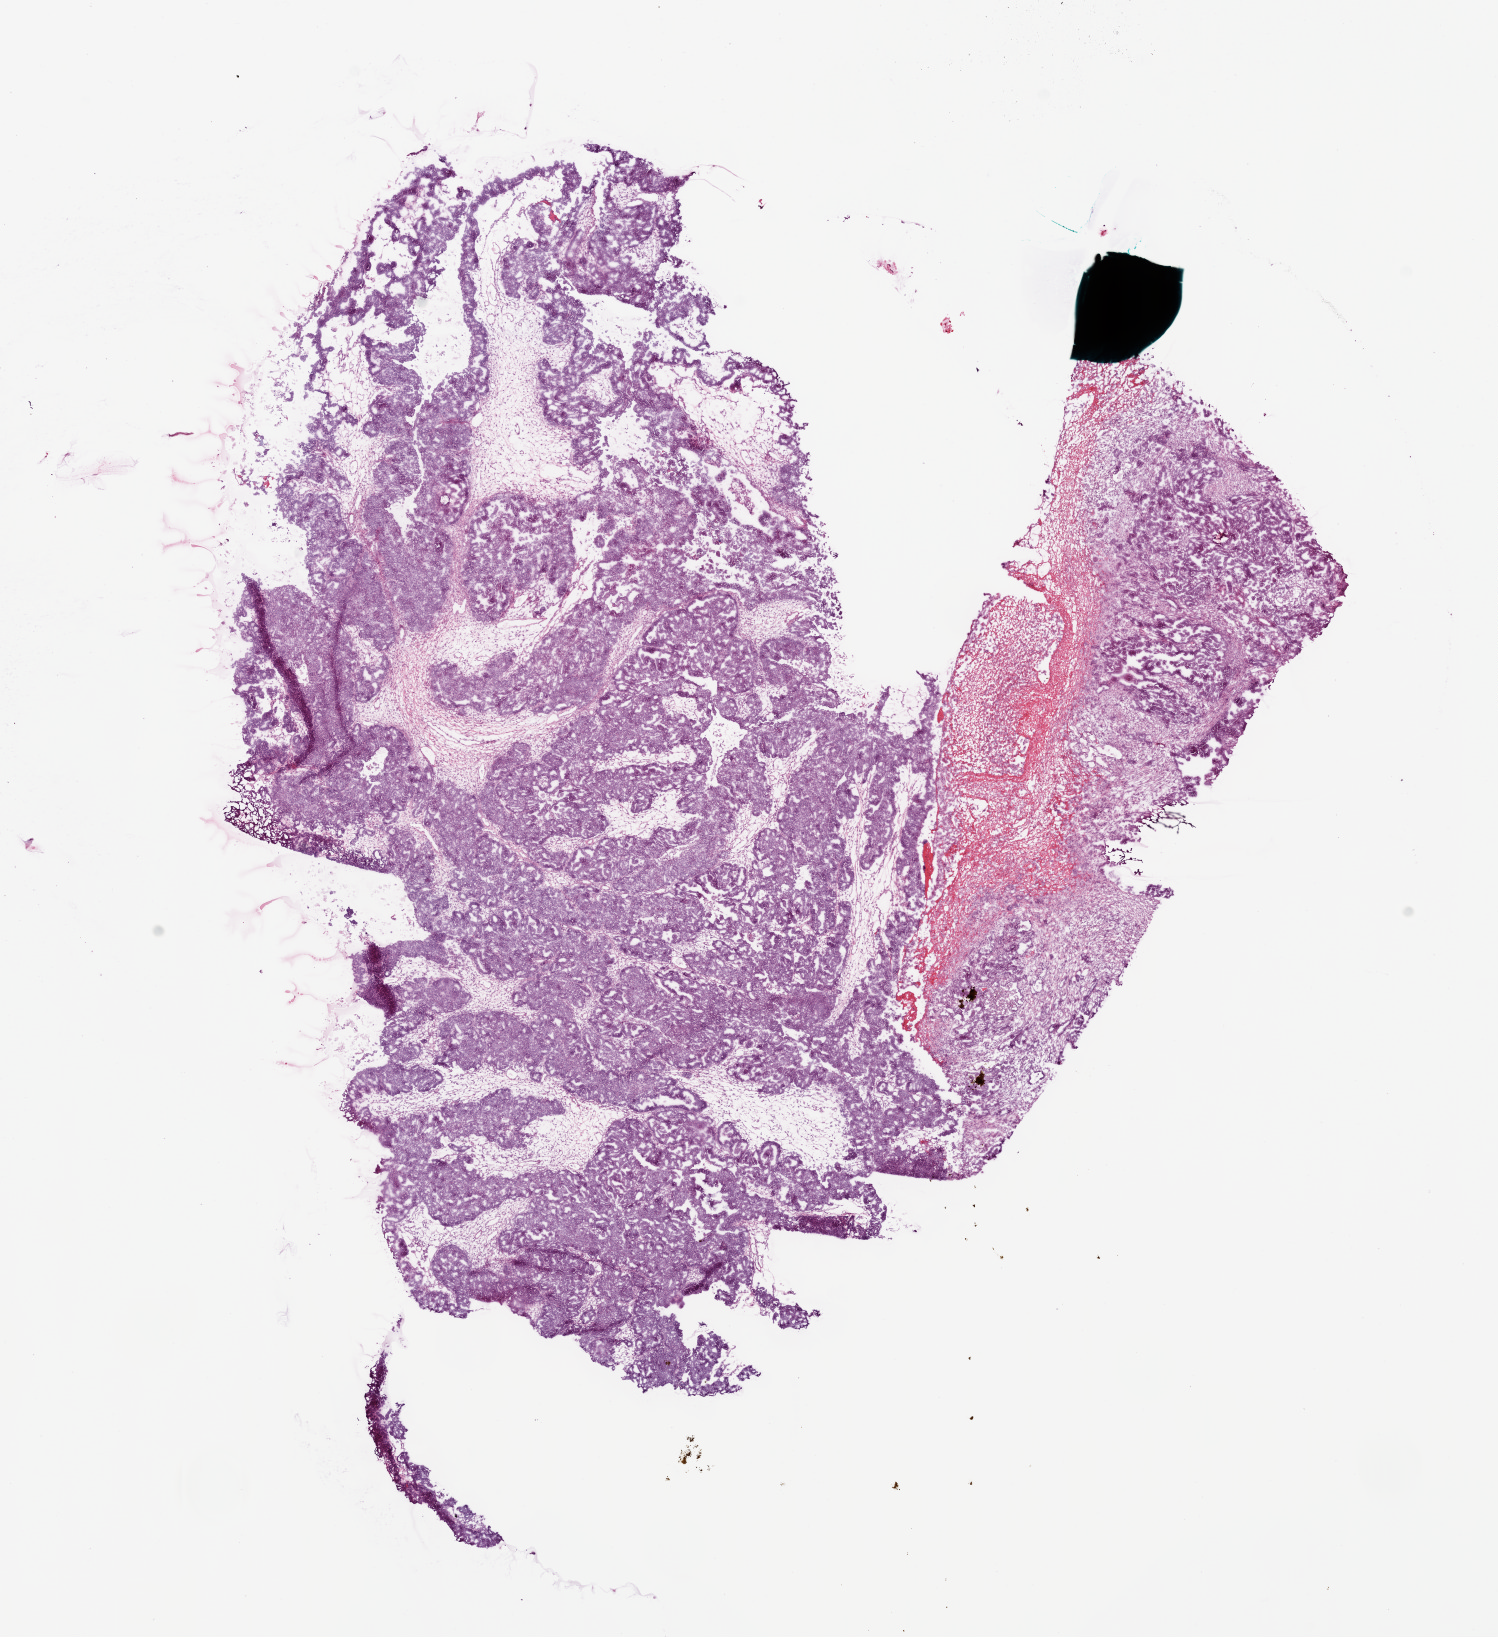
Whole-slide histology image, H&E, low-resolution overview of the scanned area, about 12.1 x 13.2 mm, frozen section, sample: primary tumour, ovary. Female, age 44 years at initial diagnosis. Histologic grade: G3 (poorly differentiated). Pathologist review of this section (percent, as recorded): tumour cells 75%, tumour nuclei 80%, normal cells 5%, stromal cells 20%, necrosis 0%.
- FIGO stage: IIIC
- pathologic diagnosis: Serous cystadenocarcinoma, NOS